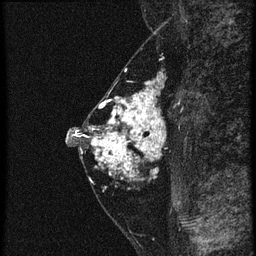
Breast MRI (dynamic contrast-enhanced), one sagittal slice. Slice 28 of 60 in the series (ordered by position). 4 images stored at this slice position (order not interpretable as contrast timing). 1.5 T. TE 4.2 ms, TR 20.4 ms. 256 × 256 image matrix, field of view 180 × 180 mm. Patient: female, 46 years. Case-level facts recorded for this patient, not image findings: setting: breast cancer imaged before/during neoadjuvant chemotherapy; receptor status: triple-negative.
Annotated regions visible in this slice (semi-automatic segmentation, software-assisted and operator-edited):
- analysis volume of interest (the breast-tissue region the enhancement analysis was run in; not a lesion): box from (x=88, y=82) to (x=171, y=185) px
- tumour enhancement mask (voxels above the 90 % enhancement threshold inside the analysis volume of interest): (x=90, y=82)–(x=165, y=177)